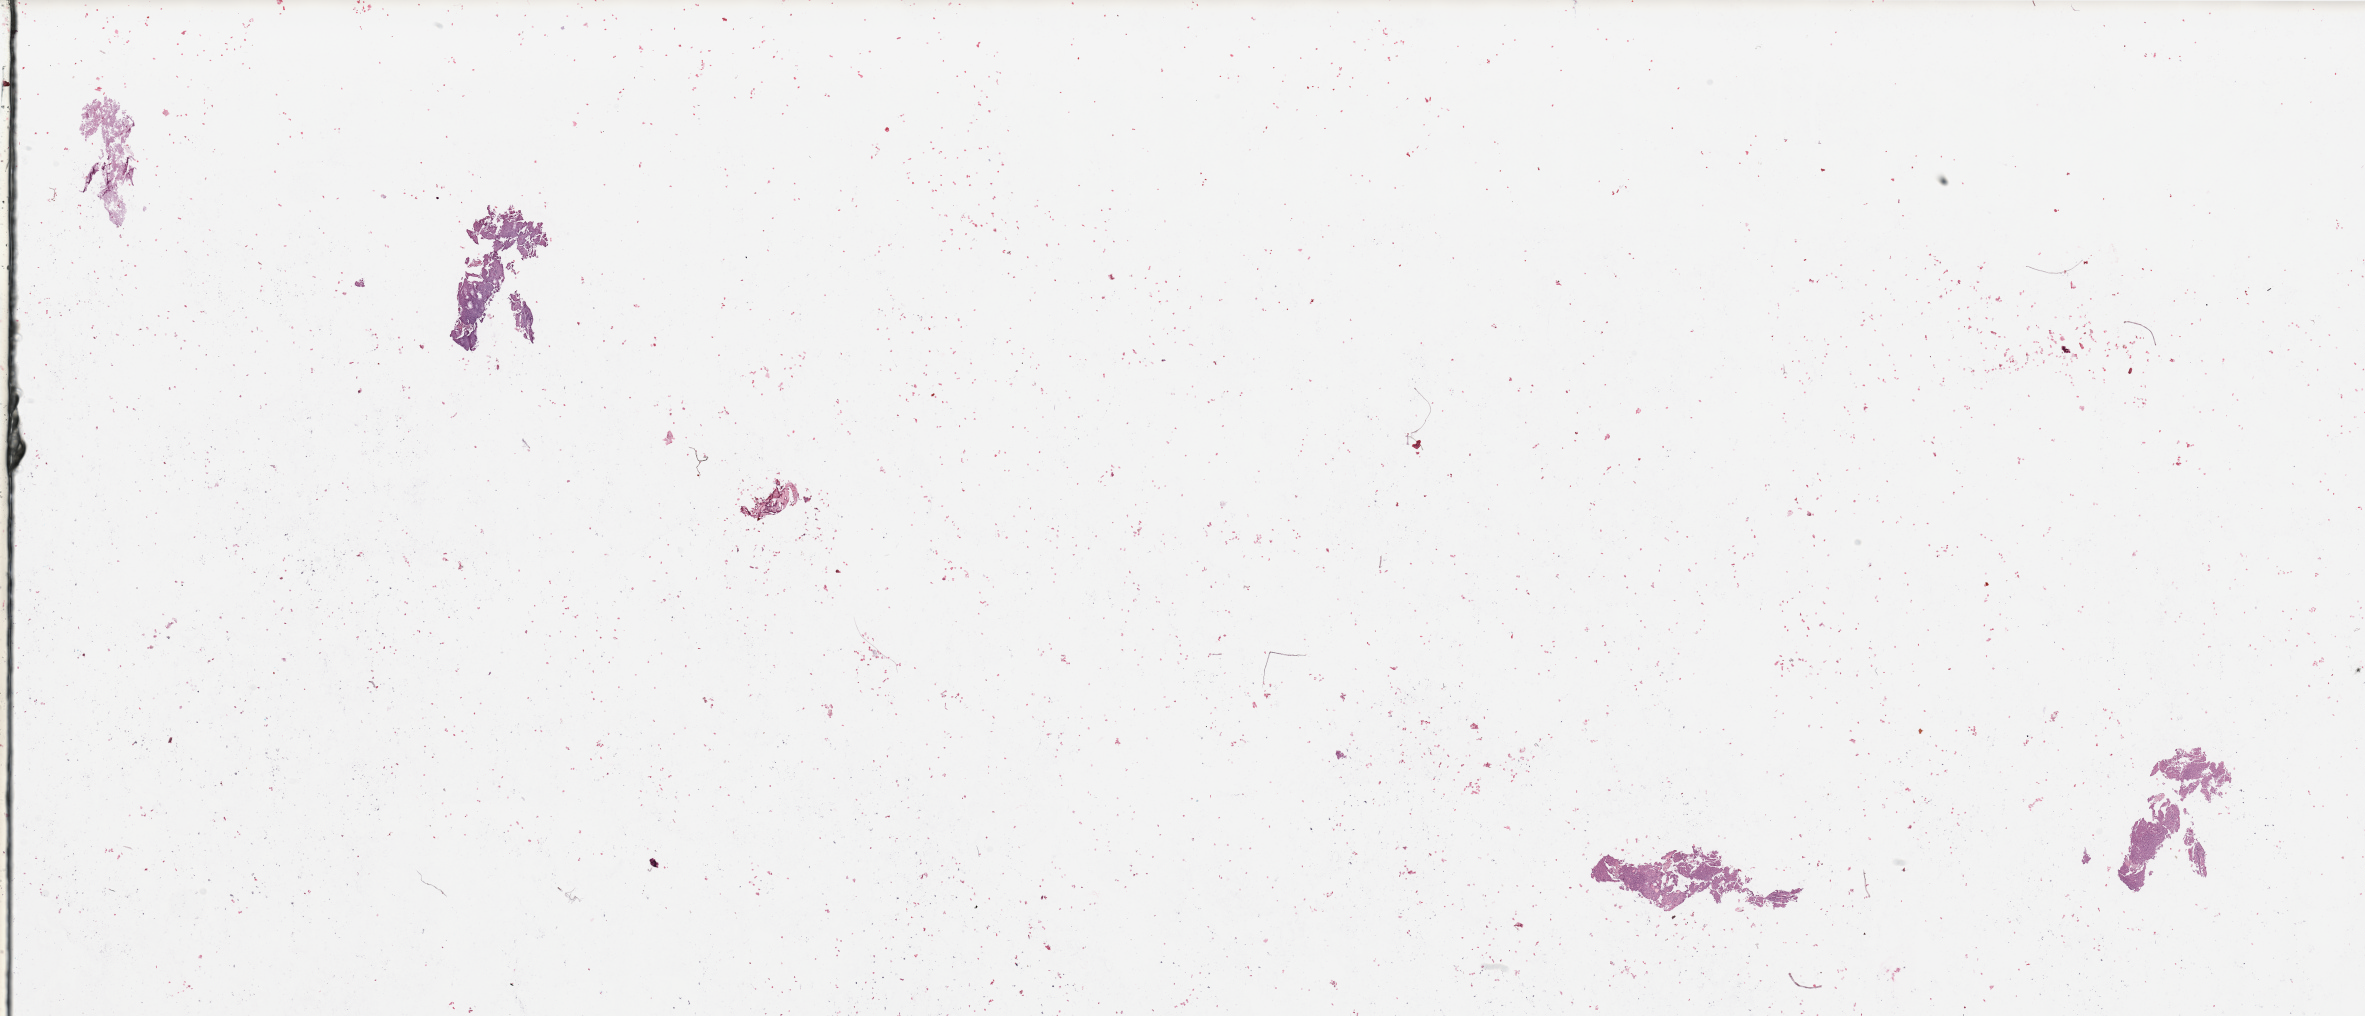
Whole-slide histology image, H&E — a low-resolution overview of the entire scanned area, about 37.4 x 16.1 mm (slide scanned at 20x); uterus, tumour tissue. Patient: female, age 77 years.
Diagnosis: Endometrioid adenocarcinoma, NOS.